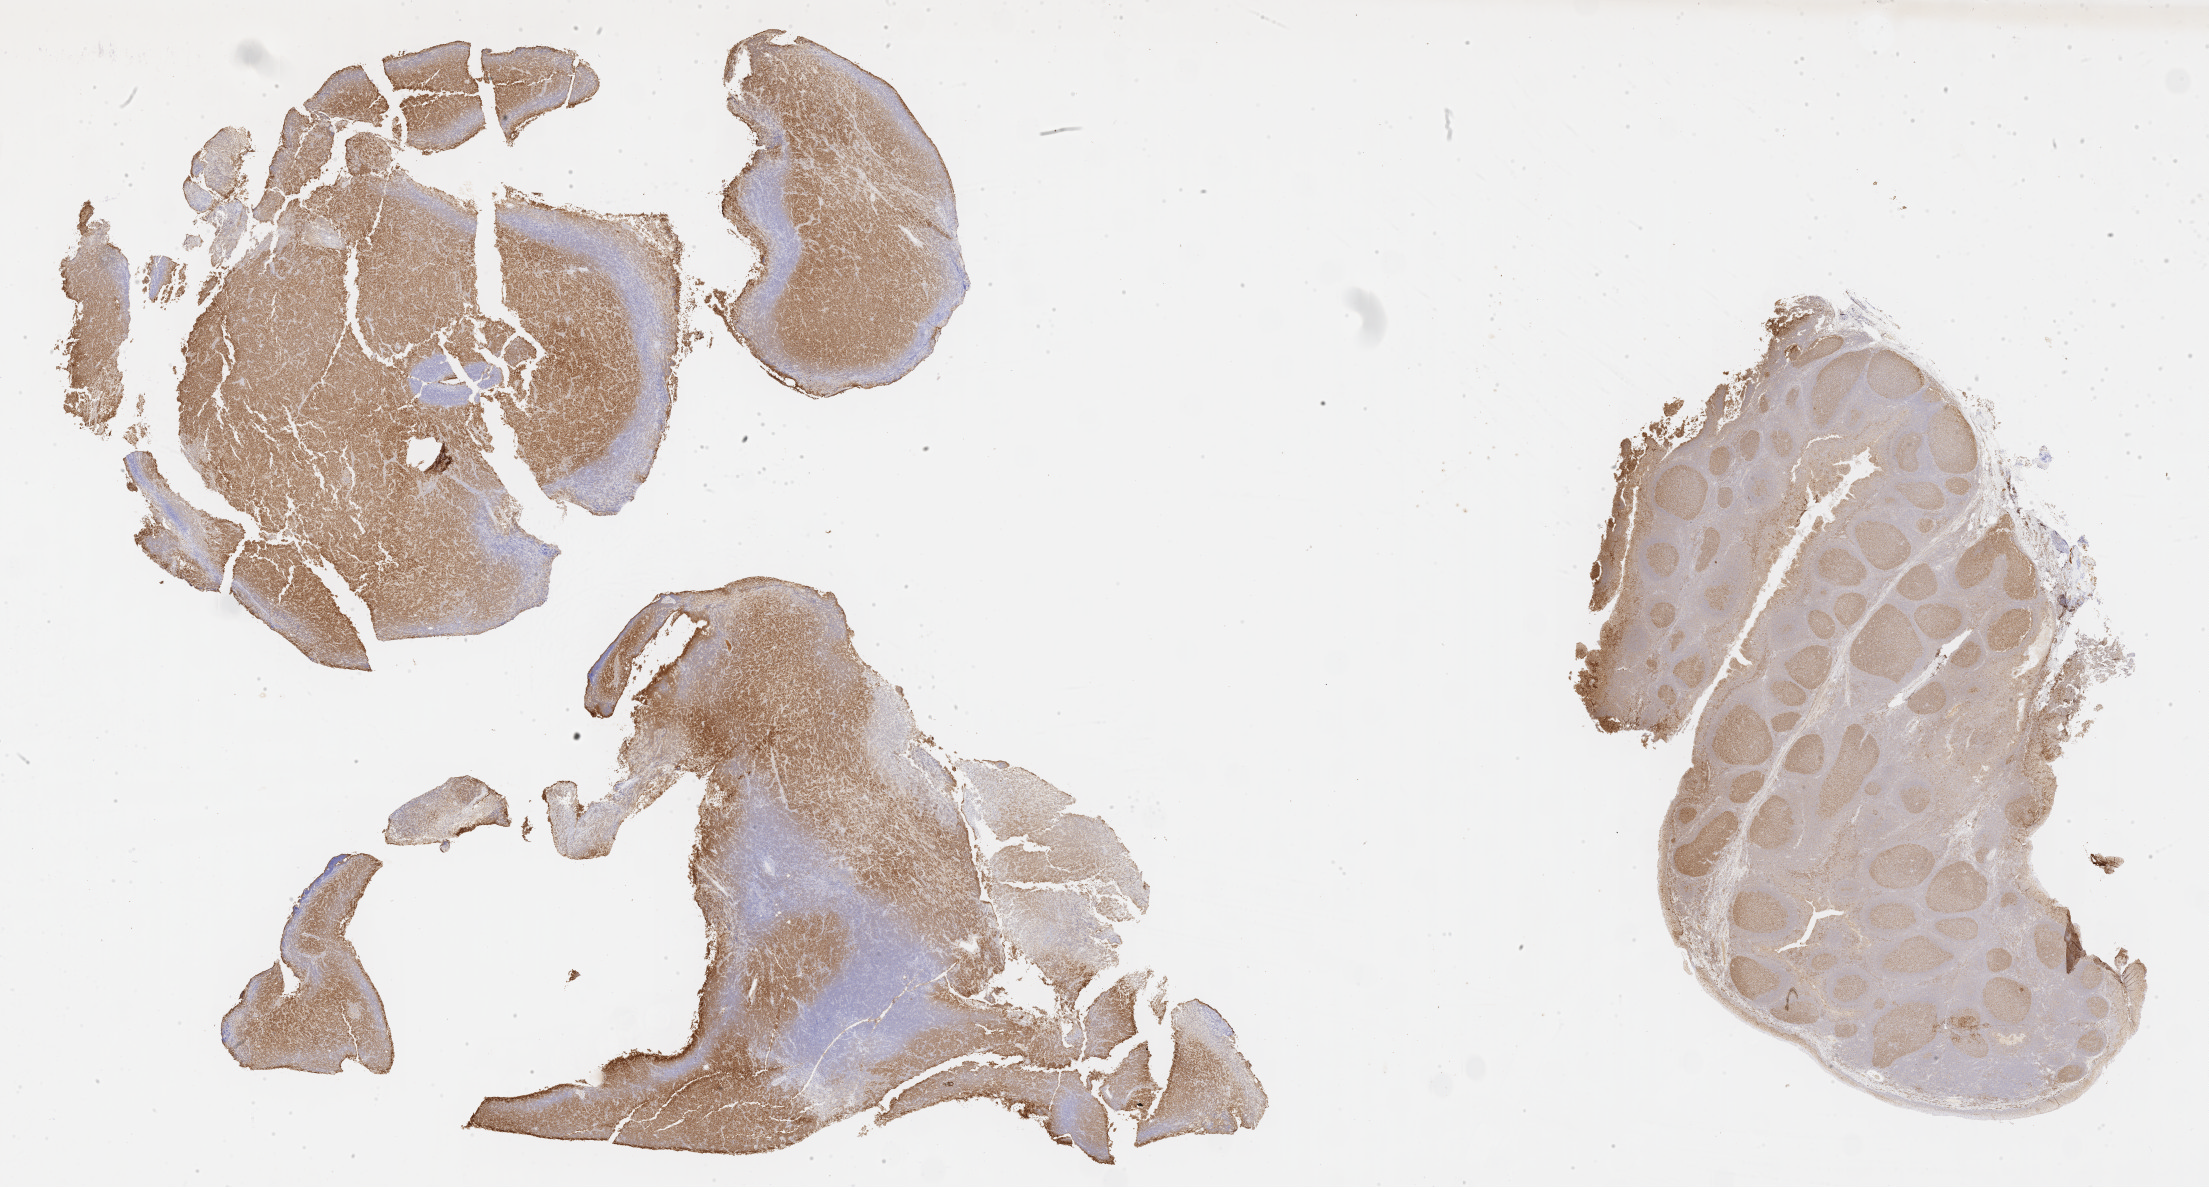
Immunohistochemistry (IHC) whole-slide image stained for BCL6 — whole scanned area (about 35.7 x 19.2 mm) shown as a low-resolution overview. Specimen: tumor tissue. Anatomic site: liver. Male patient, age 45 years.
* diagnosis: Diffuse large B-cell lymphoma, NOS